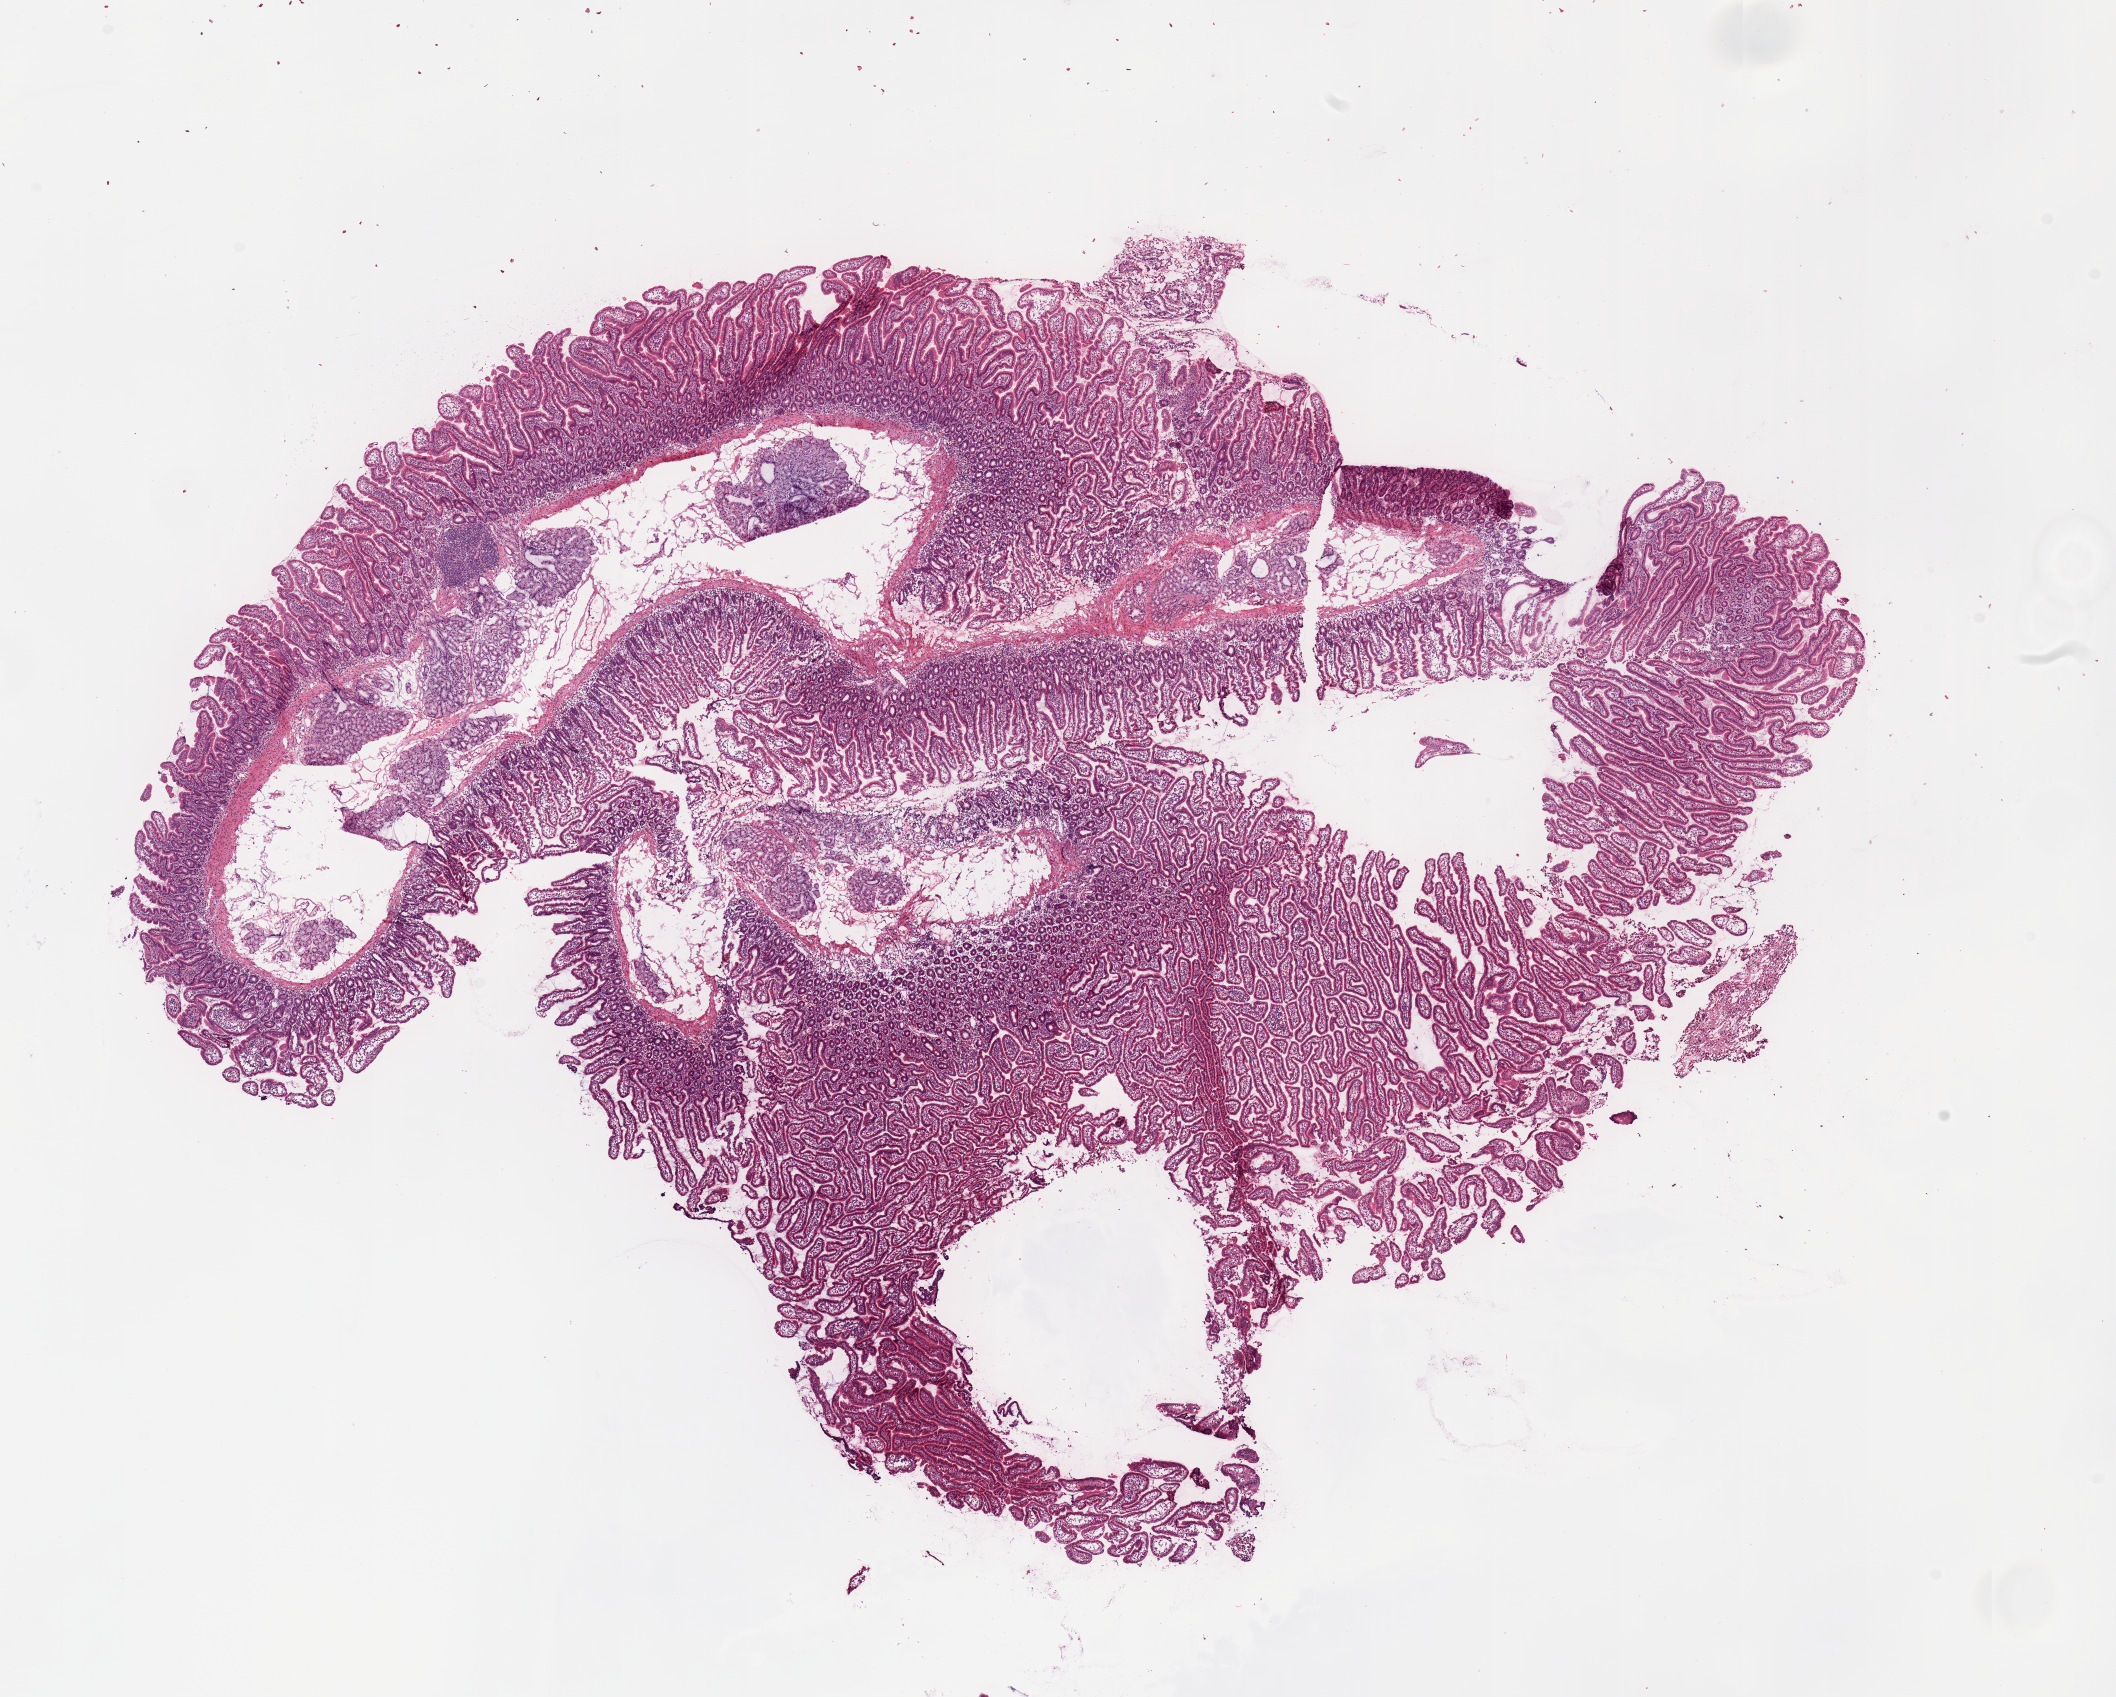
Hematoxylin and eosin (H&E) stained whole-slide image, a low-resolution overview of the entire scanned area, about 16.7 x 13.4 mm (from a 20x scan); normal (non-tumour) tissue sample, sampled site: pancreas. Patient: male, age 69 years.
- this section: normal (non-tumour) tissue from the same patient
- patient diagnosis: Infiltrating duct carcinoma, NOS